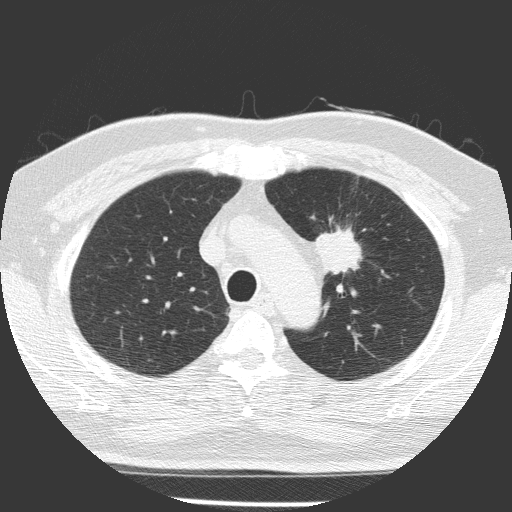
Low-dose screening chest CT, axial slice, first (baseline) screen, lung window (W 1500 / L -600 HU), 2 mm slice thickness, 512 × 512 image matrix. Male, age 70 years at enrolment. Current smoker at enrolment.
Expert reader's lesion annotation, box from (x=298, y=221) to (x=372, y=295) px. The screening reader recorded 3 non-calcified nodules or masses ≥4 mm on this exam; which of them this box marks is not recorded. Participant outcome: lung cancer diagnosed 58 days after this screen — squamous cell carcinoma, NOS, left upper lobe, poorly differentiated (G3), stage IB (AJCC 6th edition), 47 mm at pathology.